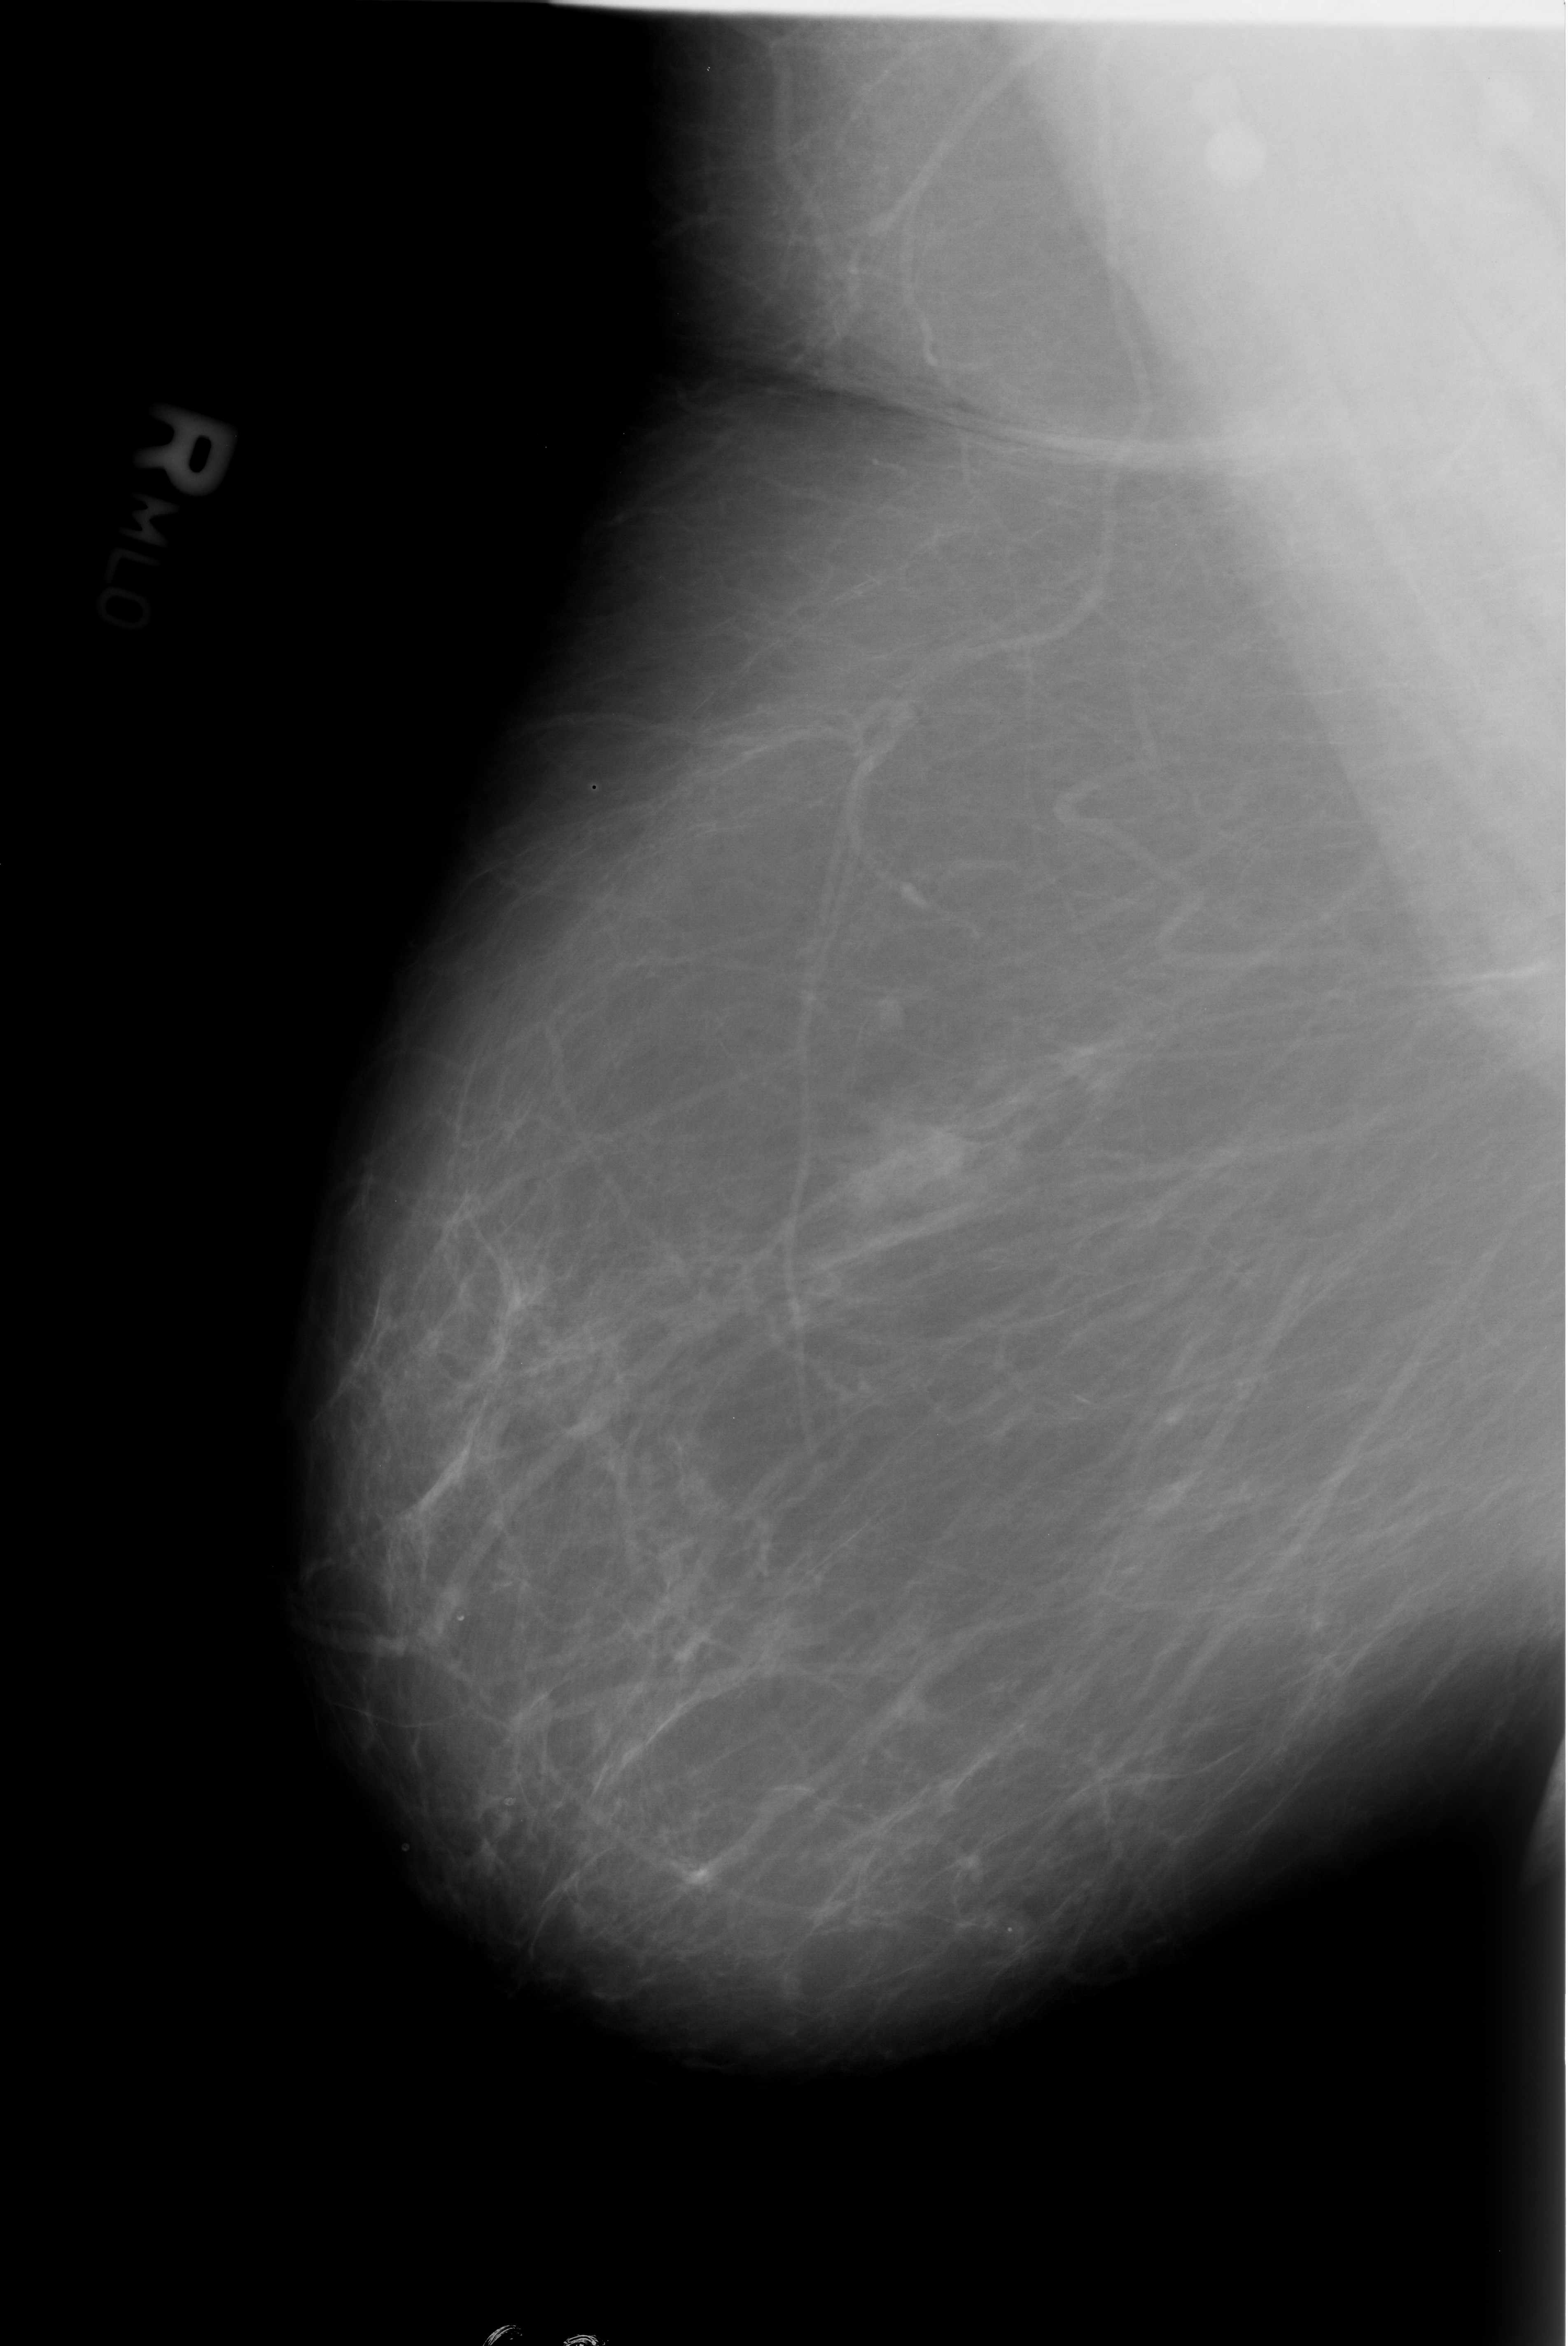
Digitized screen-film mammogram, right breast, mediolateral oblique (MLO) view, breast composition: almost entirely fatty (BI-RADS density category 1 of 4).
Radiologist-marked abnormalities on this image: mass, shape lobulated / irregular, margins microlobulated / ill defined; BI-RADS assessment category 4; subtlety rating 4 on a 1 (subtle) to 5 (obvious) scale; pathology result (as recorded, not read from the image): benign.